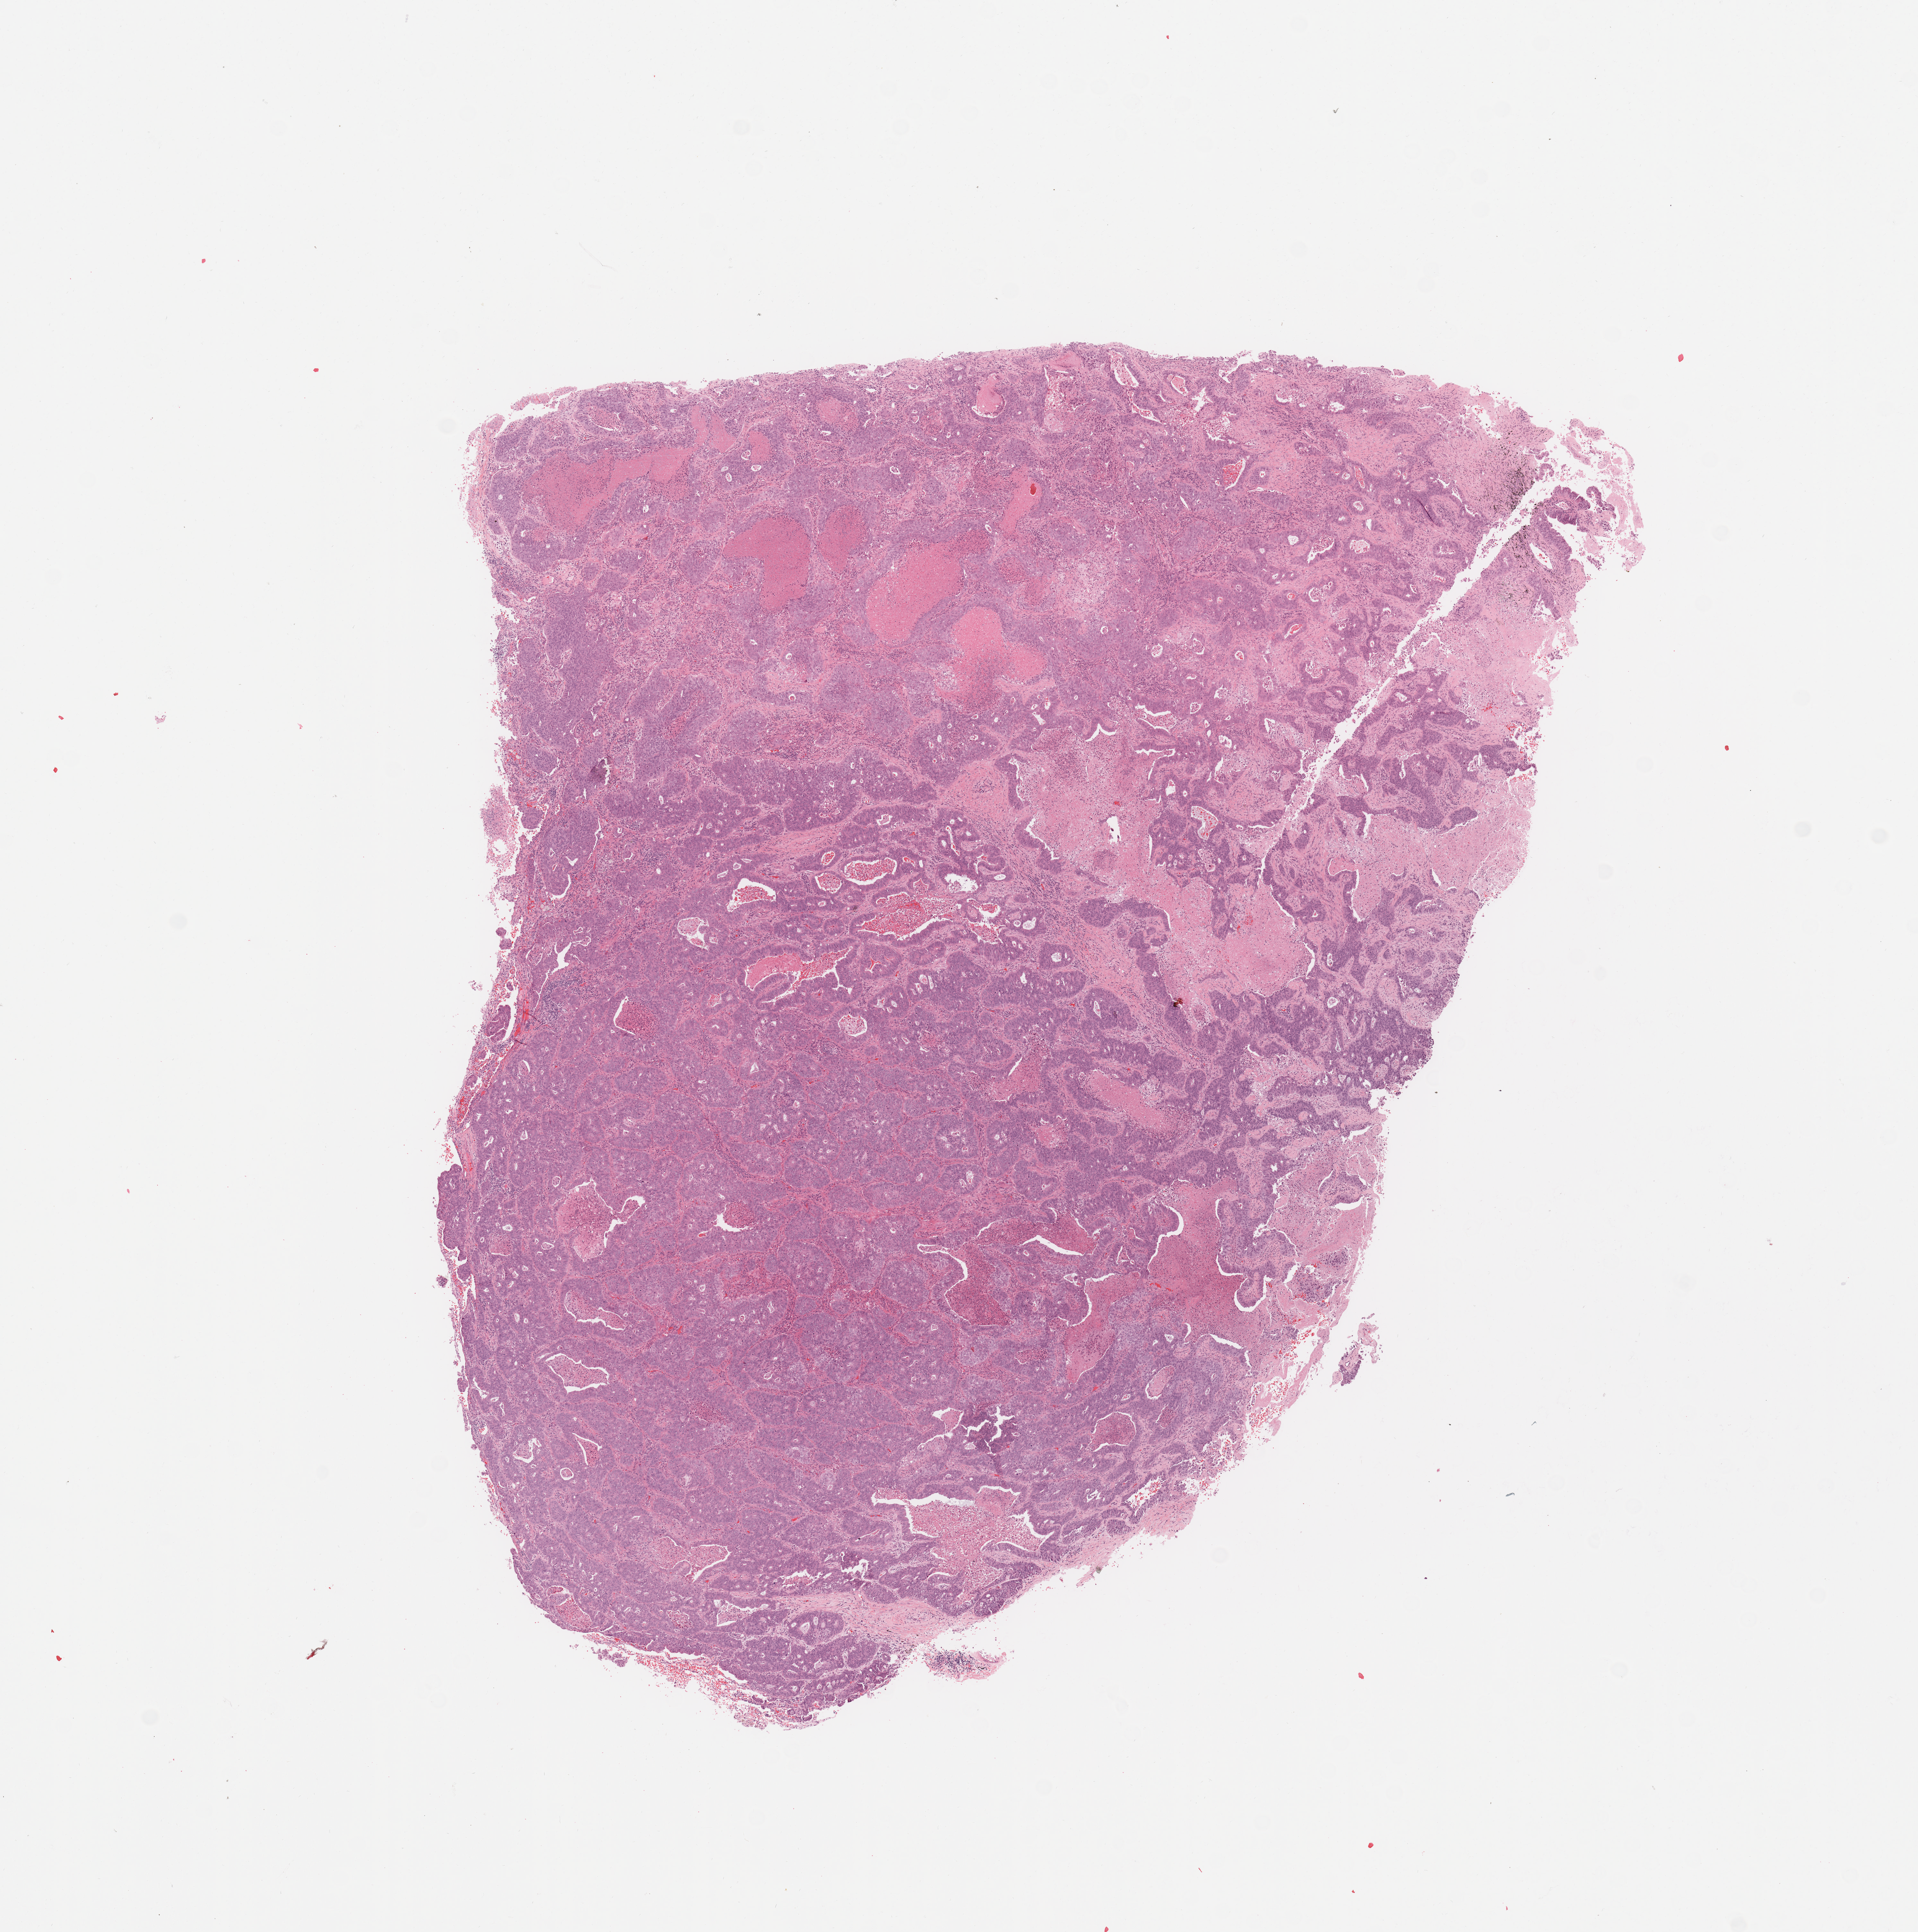
Whole-slide histology image, H&E — low-resolution overview of the scanned area, about 11.8 x 11.9 mm (from a 20x scan). Tumour tissue sample, sampled site: lung. Patient: male, age 69 years.
Histologic diagnosis: Adenocarcinoma, NOS.